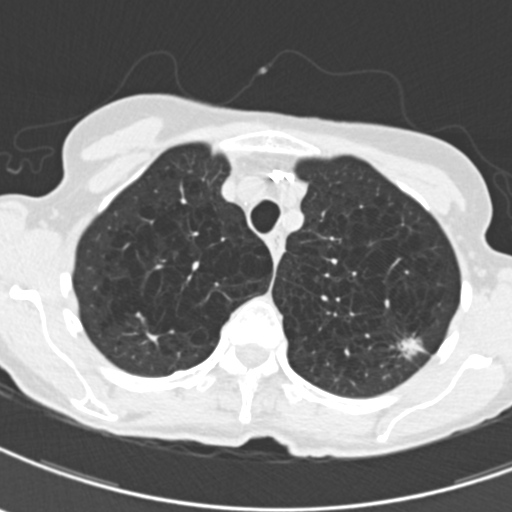
Axial slice from a low-dose chest CT screening exam. Third annual screen. Lung window (W 1500 / L -600 HU). Slice 44 of 203 in the series. 512 × 512 image matrix, field of view 279 × 279 mm. Female, age 71 years at enrolment. Current smoker at enrolment.
Expert reader's lesion annotation, bounding box (x1, y1, x2, y2) in pixels: (391, 324, 439, 367). Screening reader's record for this exam (one nodule recorded; not confirmed to be the boxed lesion): non-calcified nodule or mass ≥4 mm, left upper lobe, 12 × 9 mm, spiculated (stellate) margins, mixed attenuation, pre-existing on the prior screen: yes; interval growth: yes. Official screen result: positive, other. Later outcome: lung cancer diagnosed 114 days after this screen — adenocarcinoma, NOS, left upper lobe, moderately differentiated (G2), stage IA (AJCC 6th edition), 12 mm at pathology.